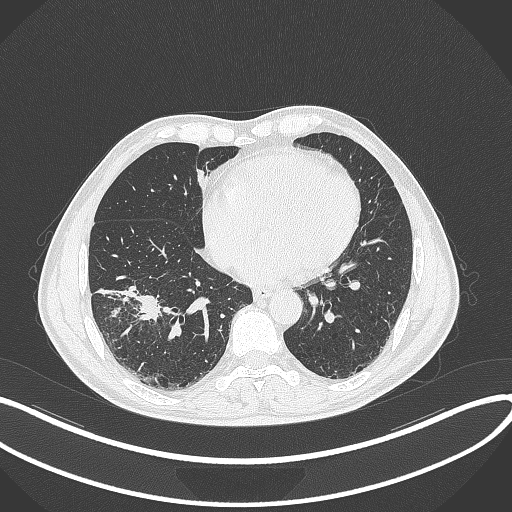
Chest CT, one axial slice. Slice 131 of 364 in the series (ordered by position). Reconstruction kernel B70f. 120 kVp. Lung window (W 1500 / L -600 HU). 512 × 512 image matrix, field of view 400 × 400 mm. Patient: male, 58 years. From the clinical record (not read from this slice): clinical TNM (as recorded): T3 N0 M0.
Annotated regions visible in this slice (rectangle marked by the reading radiologist):
- lung tumour (recorded histology: squamous cell carcinoma): box from (x=137, y=290) to (x=167, y=323) px